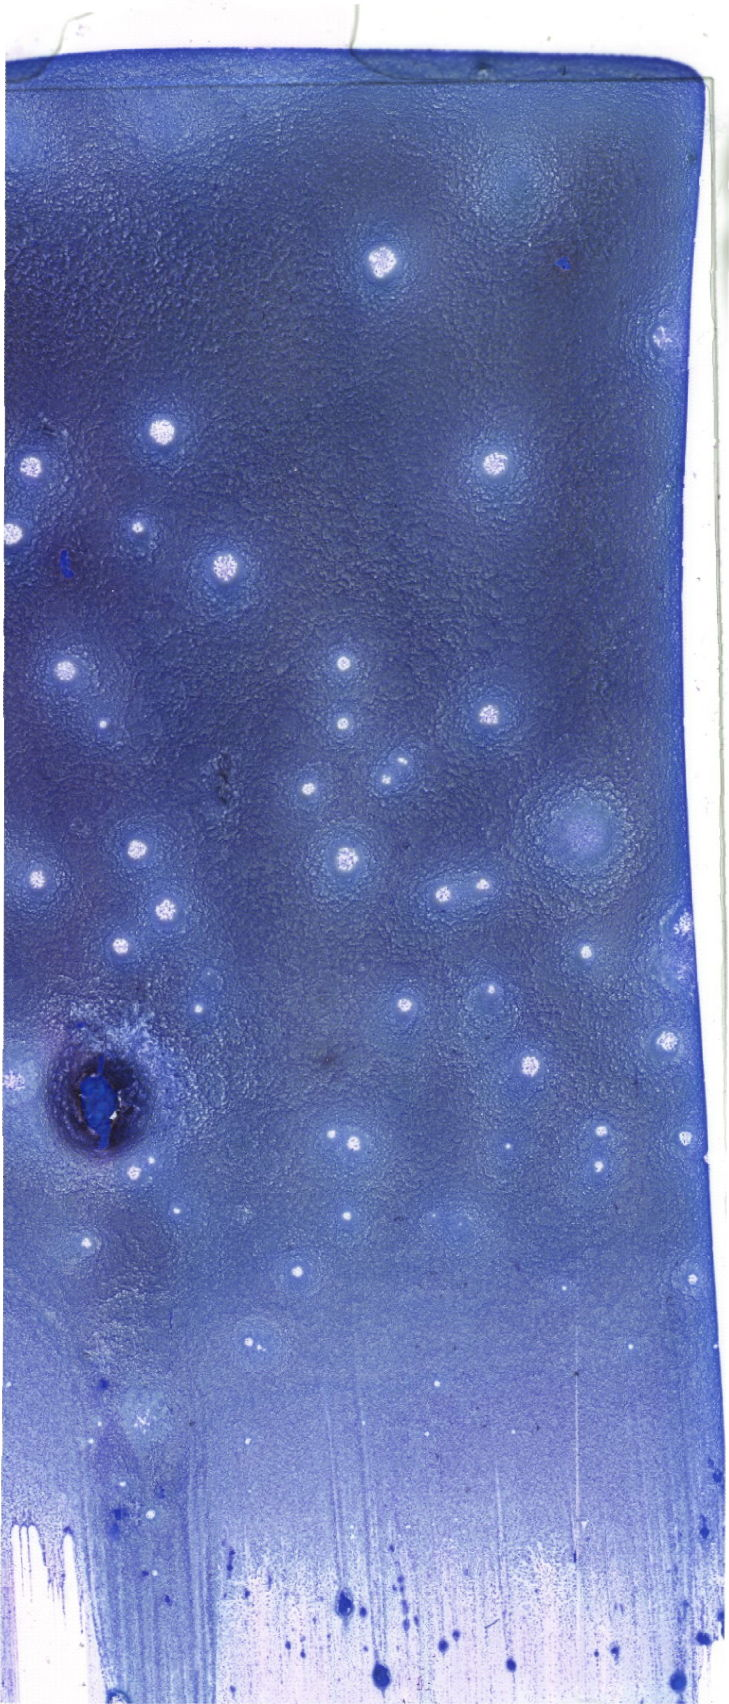
Whole-slide image of a May-Grünwald-Giemsa (MGG)-stained bone marrow aspirate smear — a low-resolution overview of the entire scanned area, about 20.7 x 48.3 mm. Patient sex: female.
Diagnosis: Acute Monocytic Leukemia.